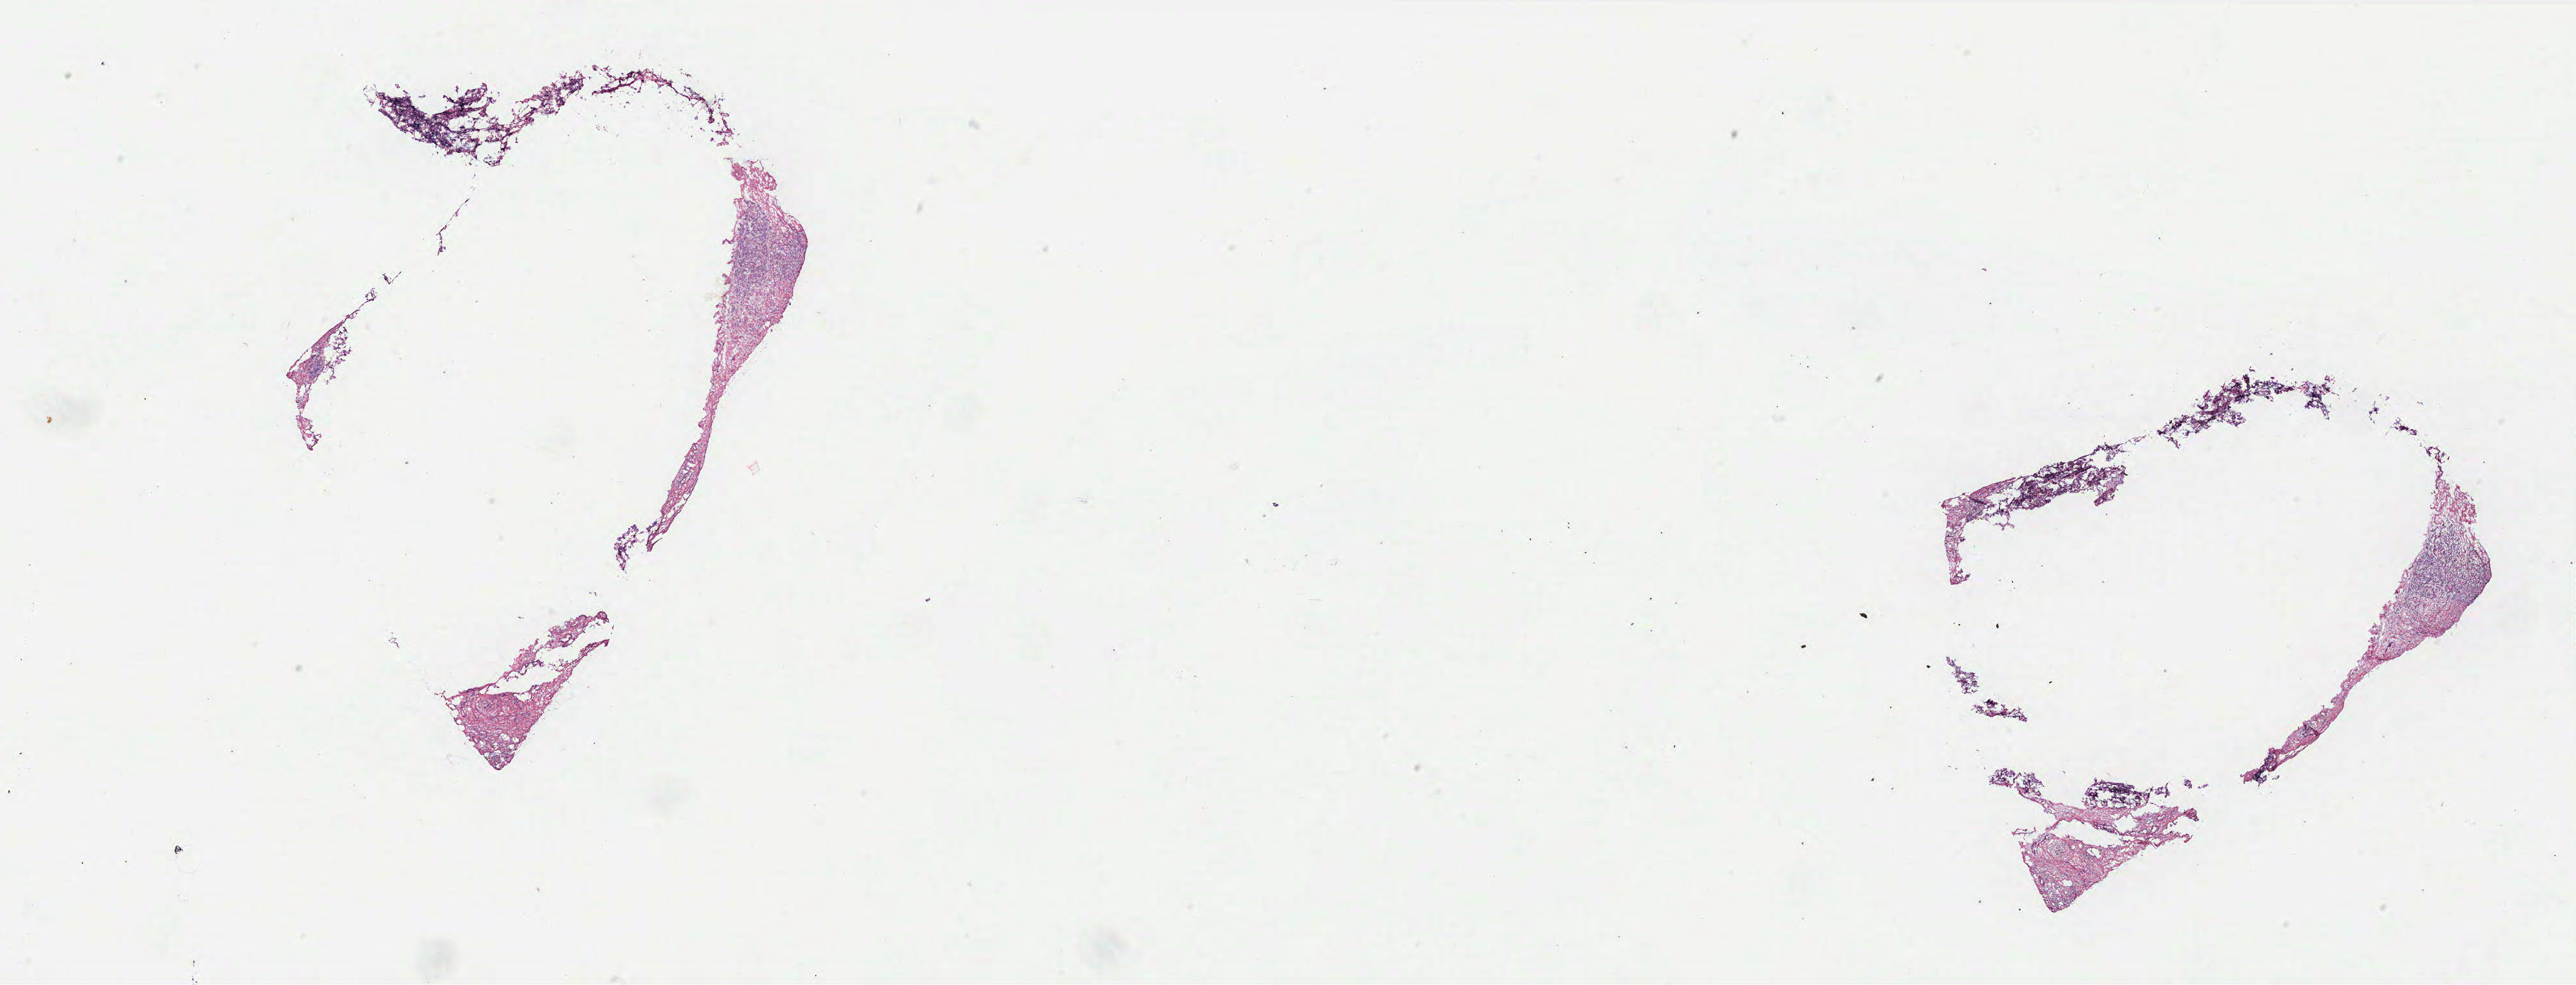
Whole-slide histology image, H&E, low-resolution overview of the scanned area, about 31.9 x 12.2 mm (acquisition: 40x scan), breast, tumour tissue. Patient: female, age 71 years.
• diagnosis: Infiltrating lobular carcinoma, NOS
• AJCC pathologic stage: IIA